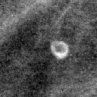
Region of interest cut from a scanned film mammogram (one marked finding); right breast; MLO view.
Marked abnormality: calcifications, morphology lucent center; BI-RADS assessment category 2; benign; no additional work-up was recommended (benign without callback).